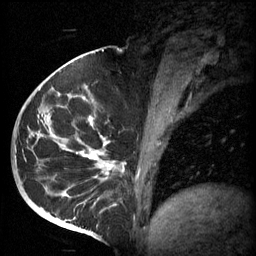
Breast MRI (dynamic contrast-enhanced), one sagittal slice. Slice 29 of 60 in the series (ordered by position). 3 images stored at this slice position (order not interpretable as contrast timing). 1.5 T. TE 4.2 ms, TR 11 ms. 256 × 256 image matrix. Female patient, age 51 years.
Annotated regions visible in this slice (semi-automatic segmentation, software-assisted and operator-edited):
- analysis volume of interest (the breast-tissue region the enhancement analysis was run in; not a lesion): bounding box (x1, y1, x2, y2) in pixels: (48, 84, 161, 197)
- tumour enhancement mask (voxels above the 70 % enhancement threshold inside the analysis volume of interest): (50, 86, 142, 197)